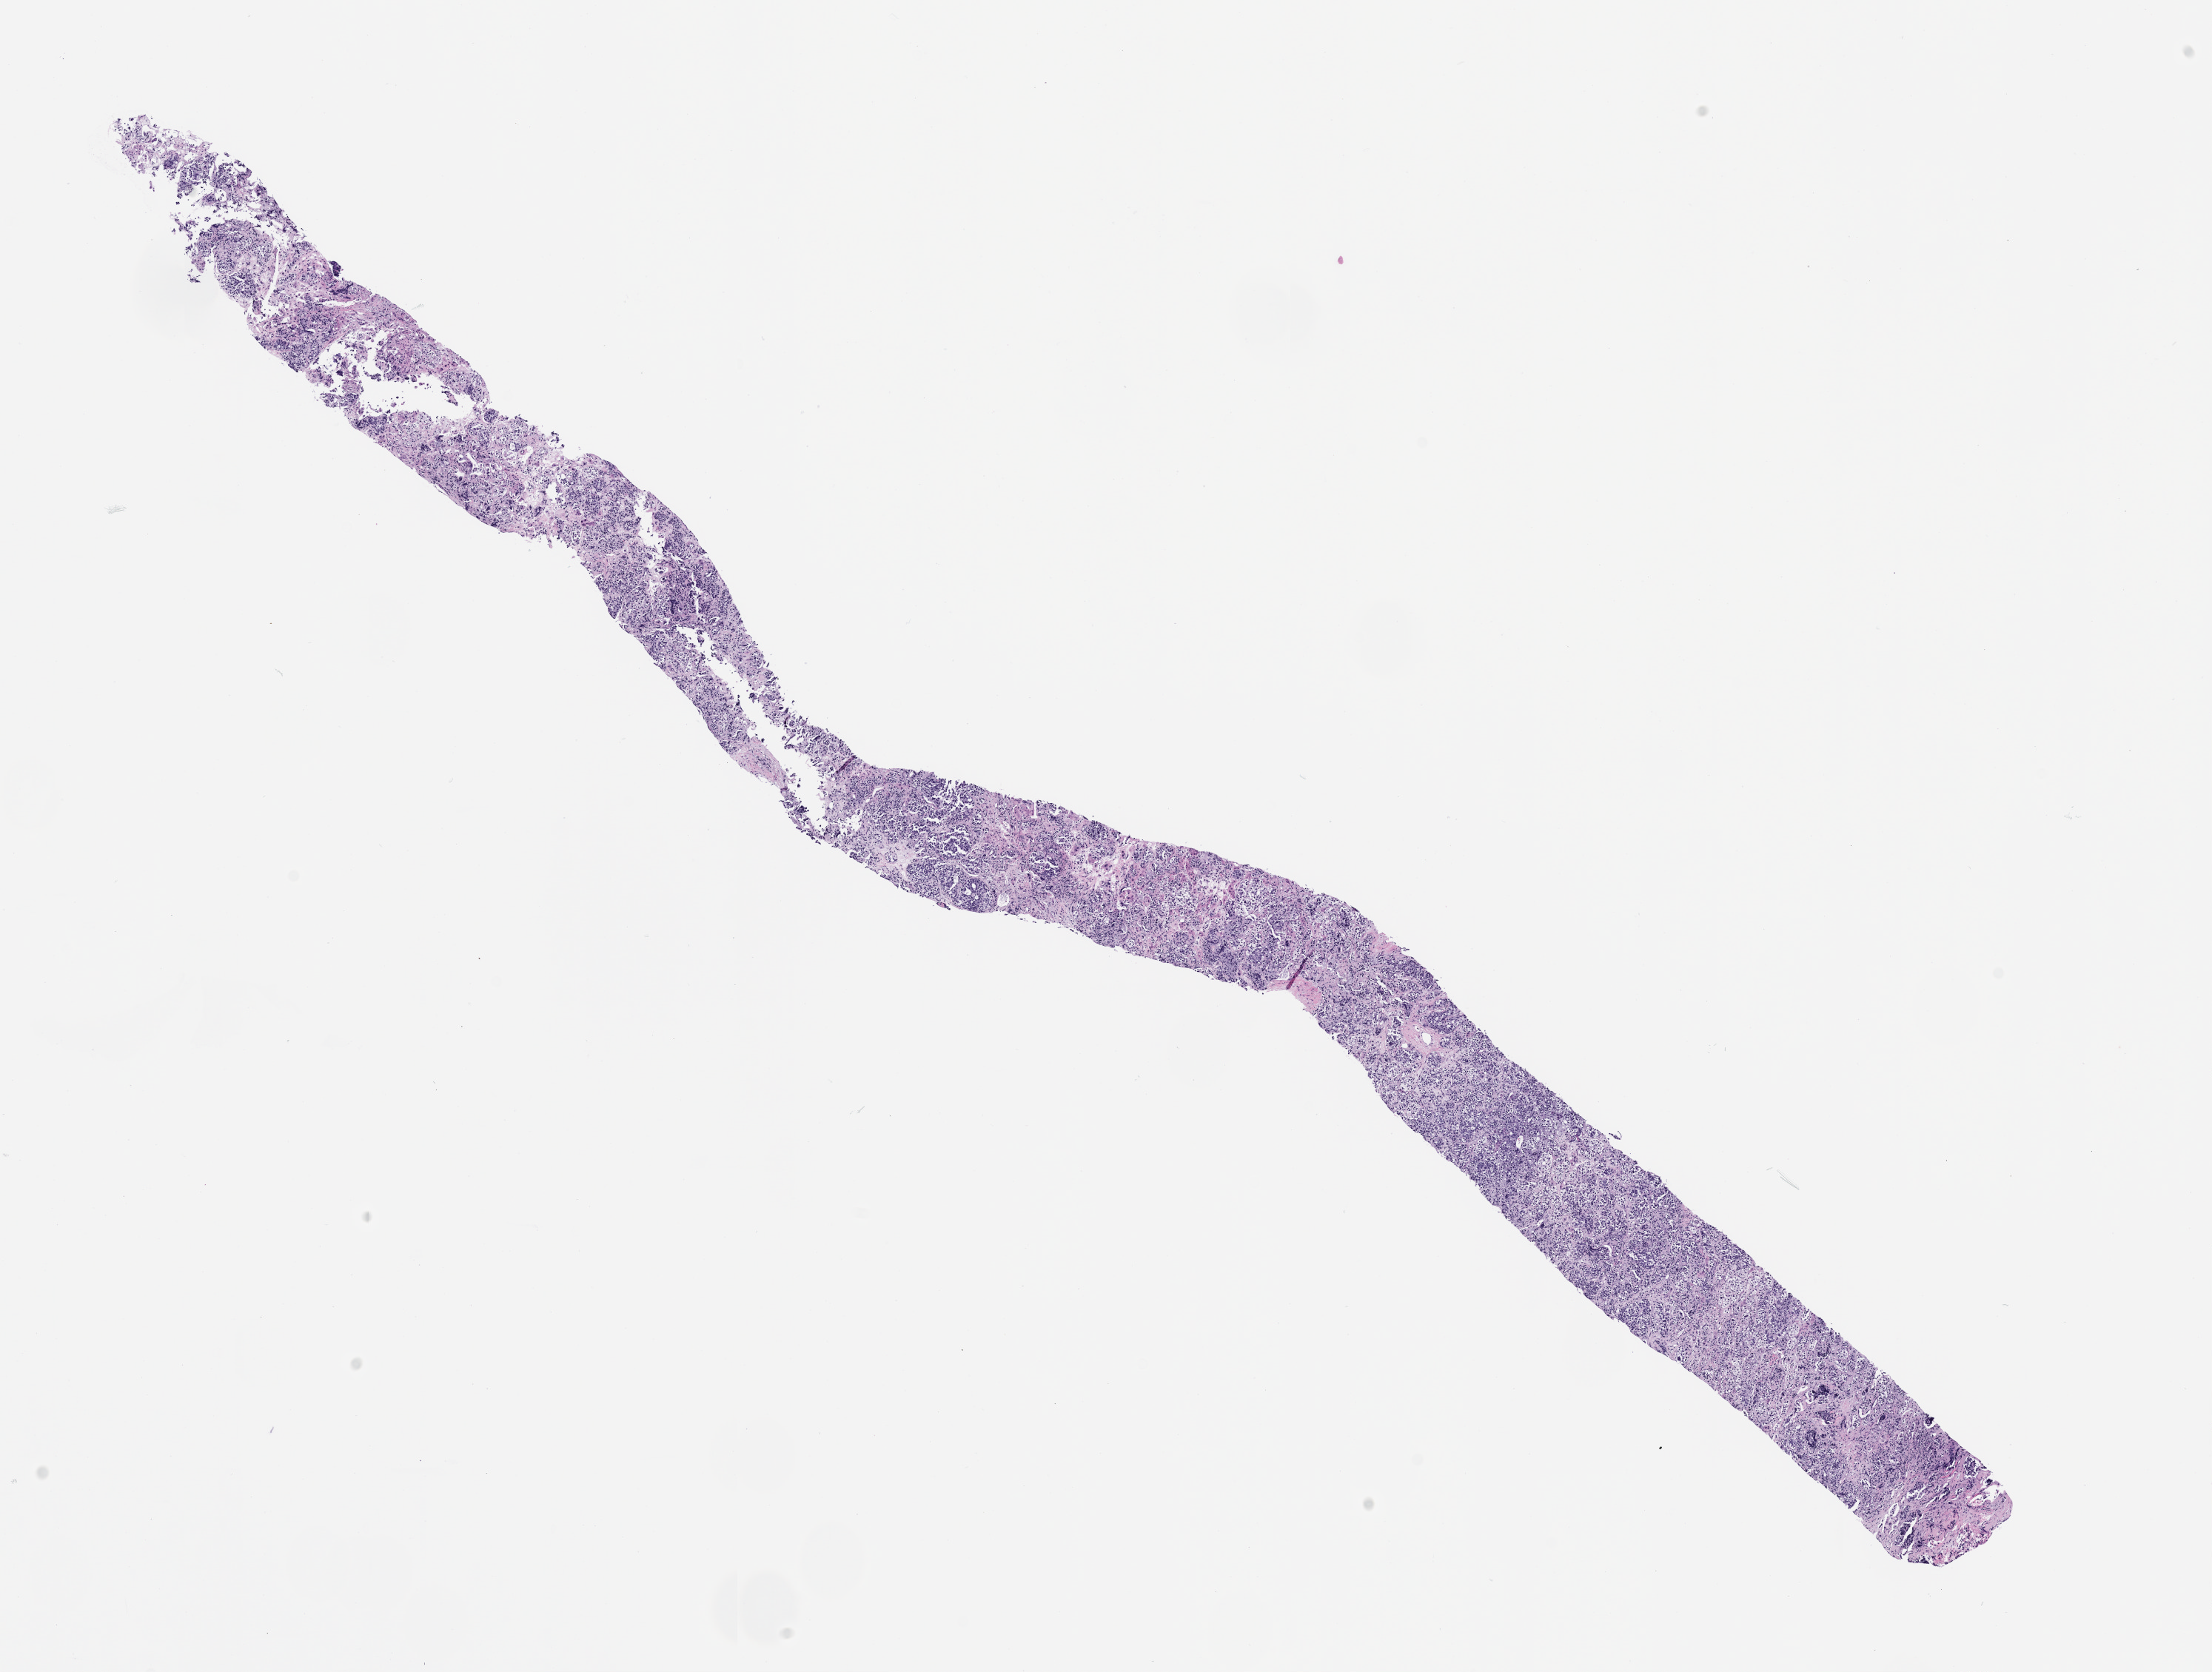
Whole-slide image, hematoxylin and eosin (H&E) stain of the patient's (originator) tumor tissue — shown as a low-resolution overview of the whole scanned area (about 12.0 x 9.1 mm); formalin-fixed paraffin-embedded section; tumor site category: prostate. Male patient.
* diagnosis: Prostate Carcinoma